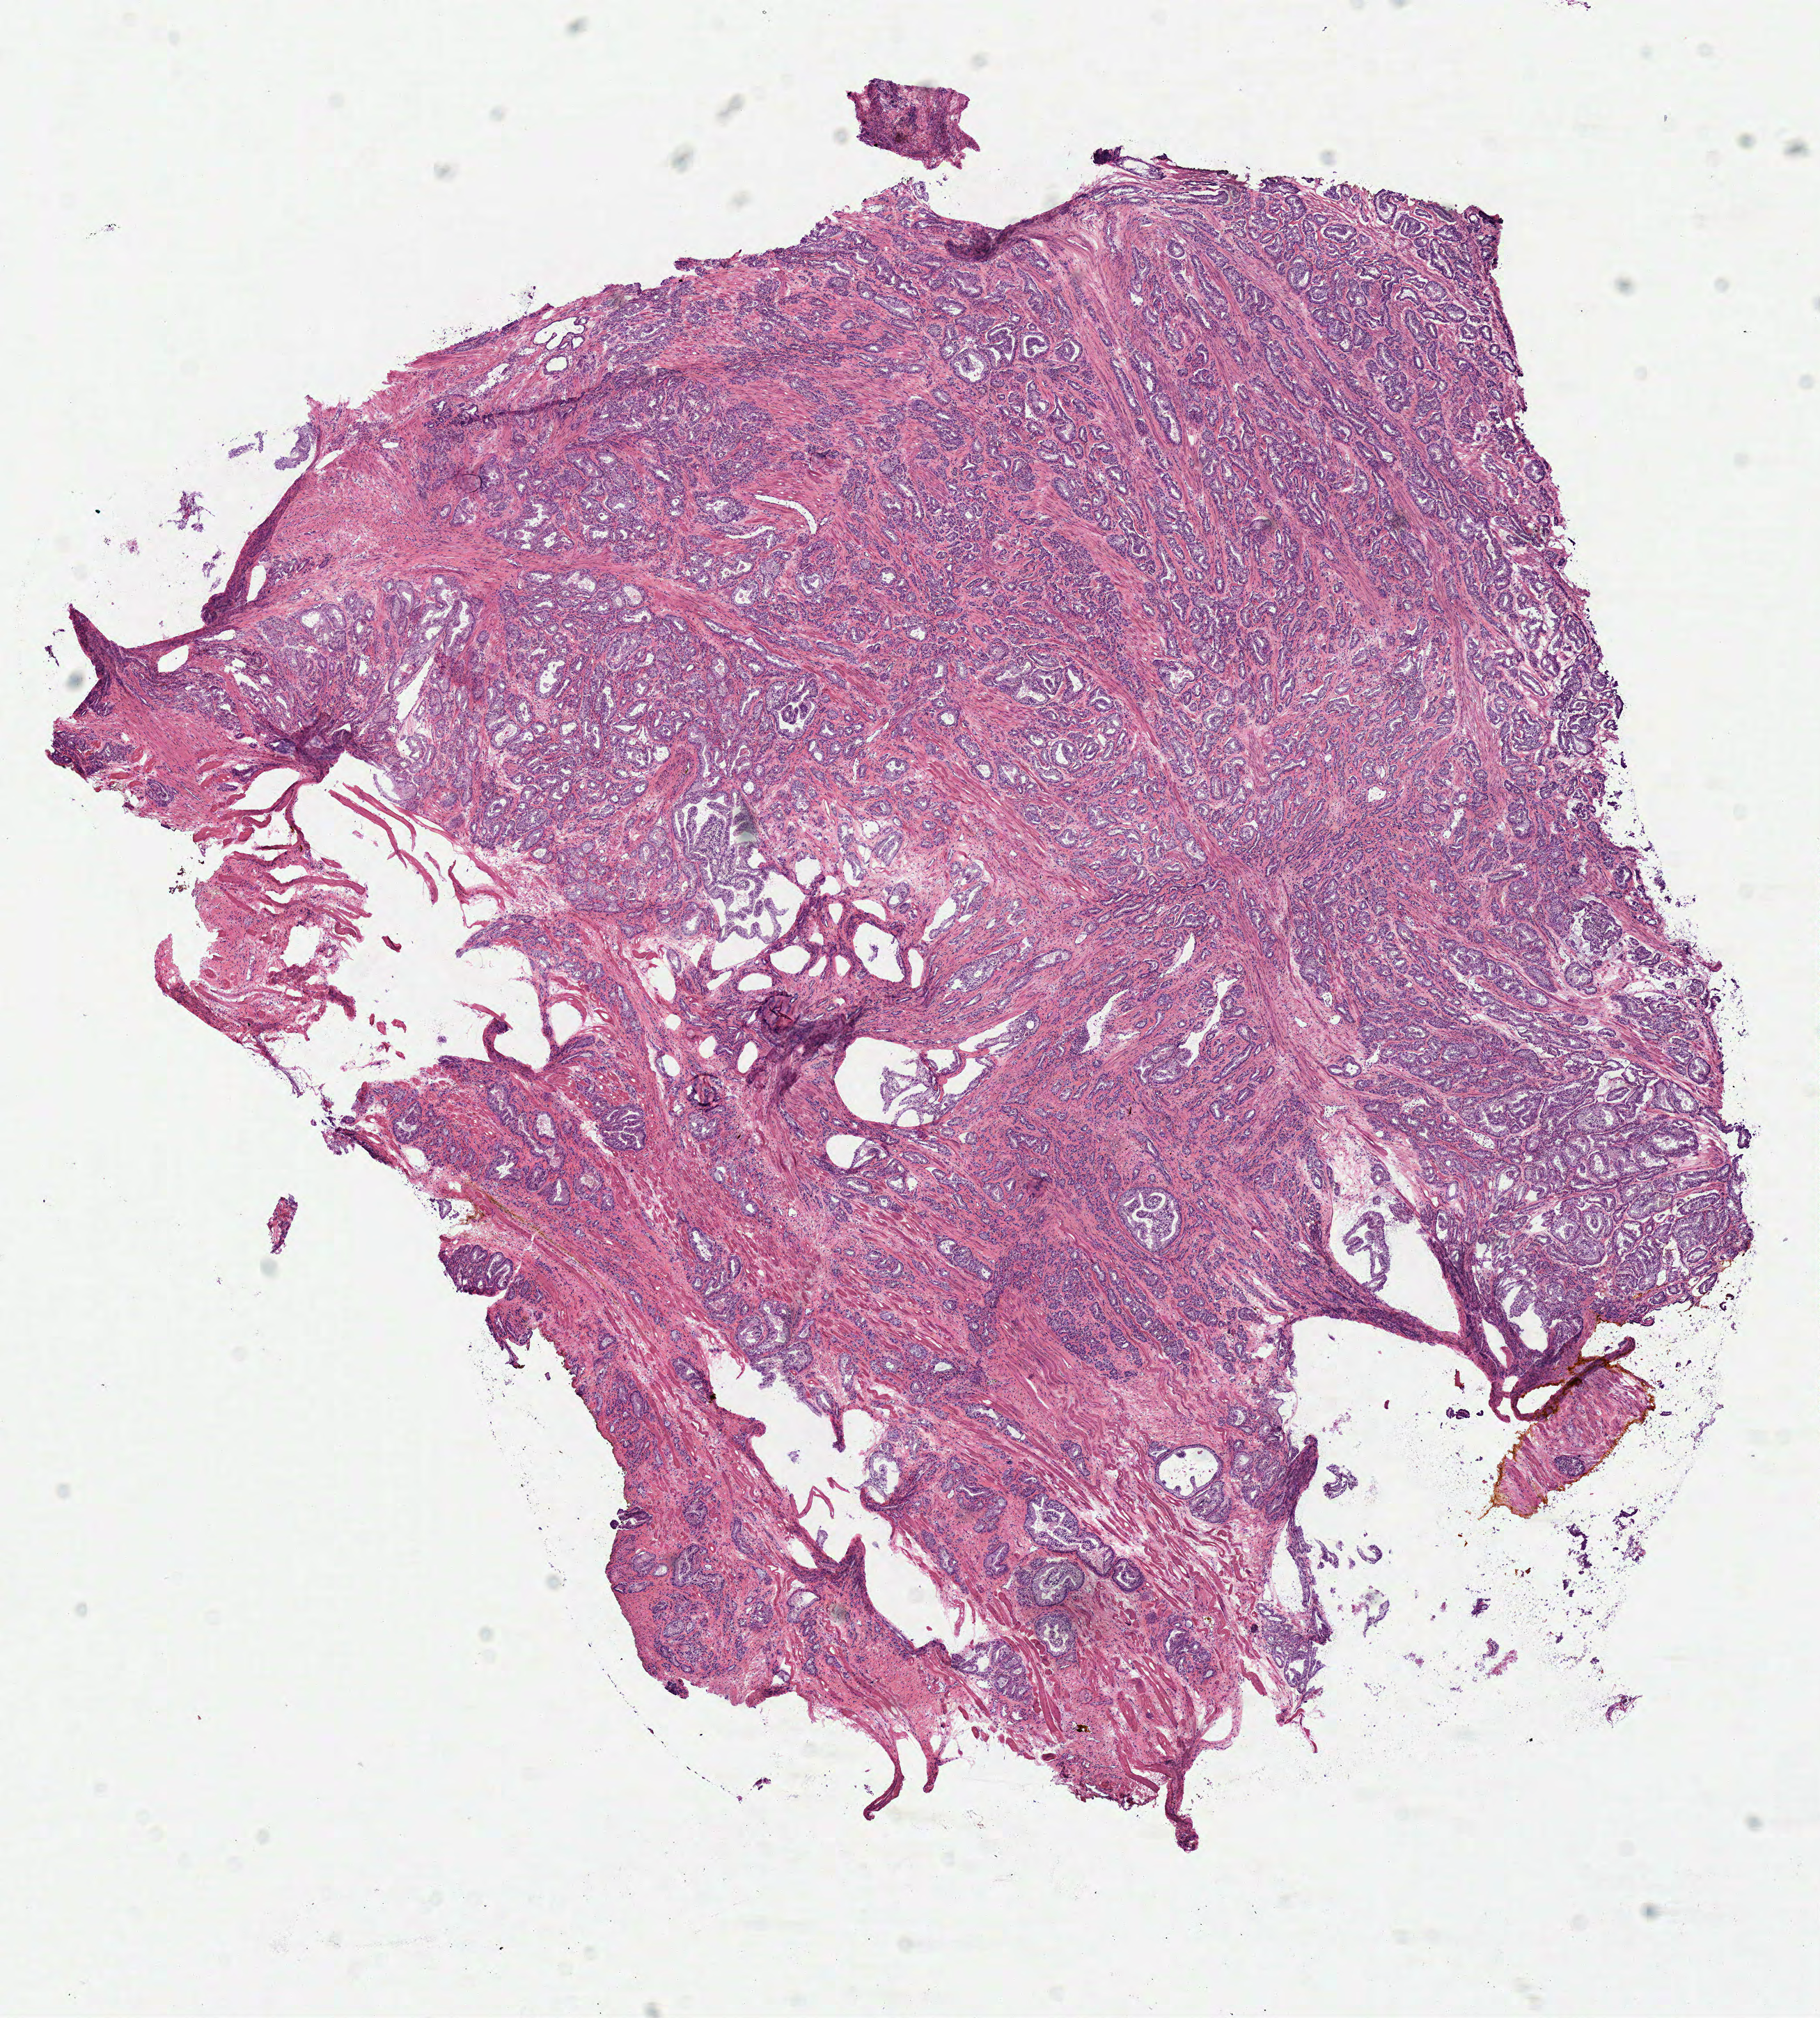
Digitized H&E tissue section (whole slide), low-resolution overview of the scanned area, about 10.3 x 11.4 mm (slide scanned at 40x), frozen section from the top of the tissue portion, primary tumour sample from the prostate. Male, age 61 years at initial diagnosis. Gleason score: 7 (4+3). Slide review estimates, as recorded: tumour cells 75%, tumour nuclei 75%, normal cells 10%, stromal cells 15%, necrosis 0%. Infiltration values recorded for this section: lymphocyte infiltration 2%, monocyte infiltration 0%, neutrophil infiltration 0%.
Lymph nodes positive (case pathology): 0 of 2 examined. Histologic diagnosis: Acinar cell carcinoma (prostate gland).